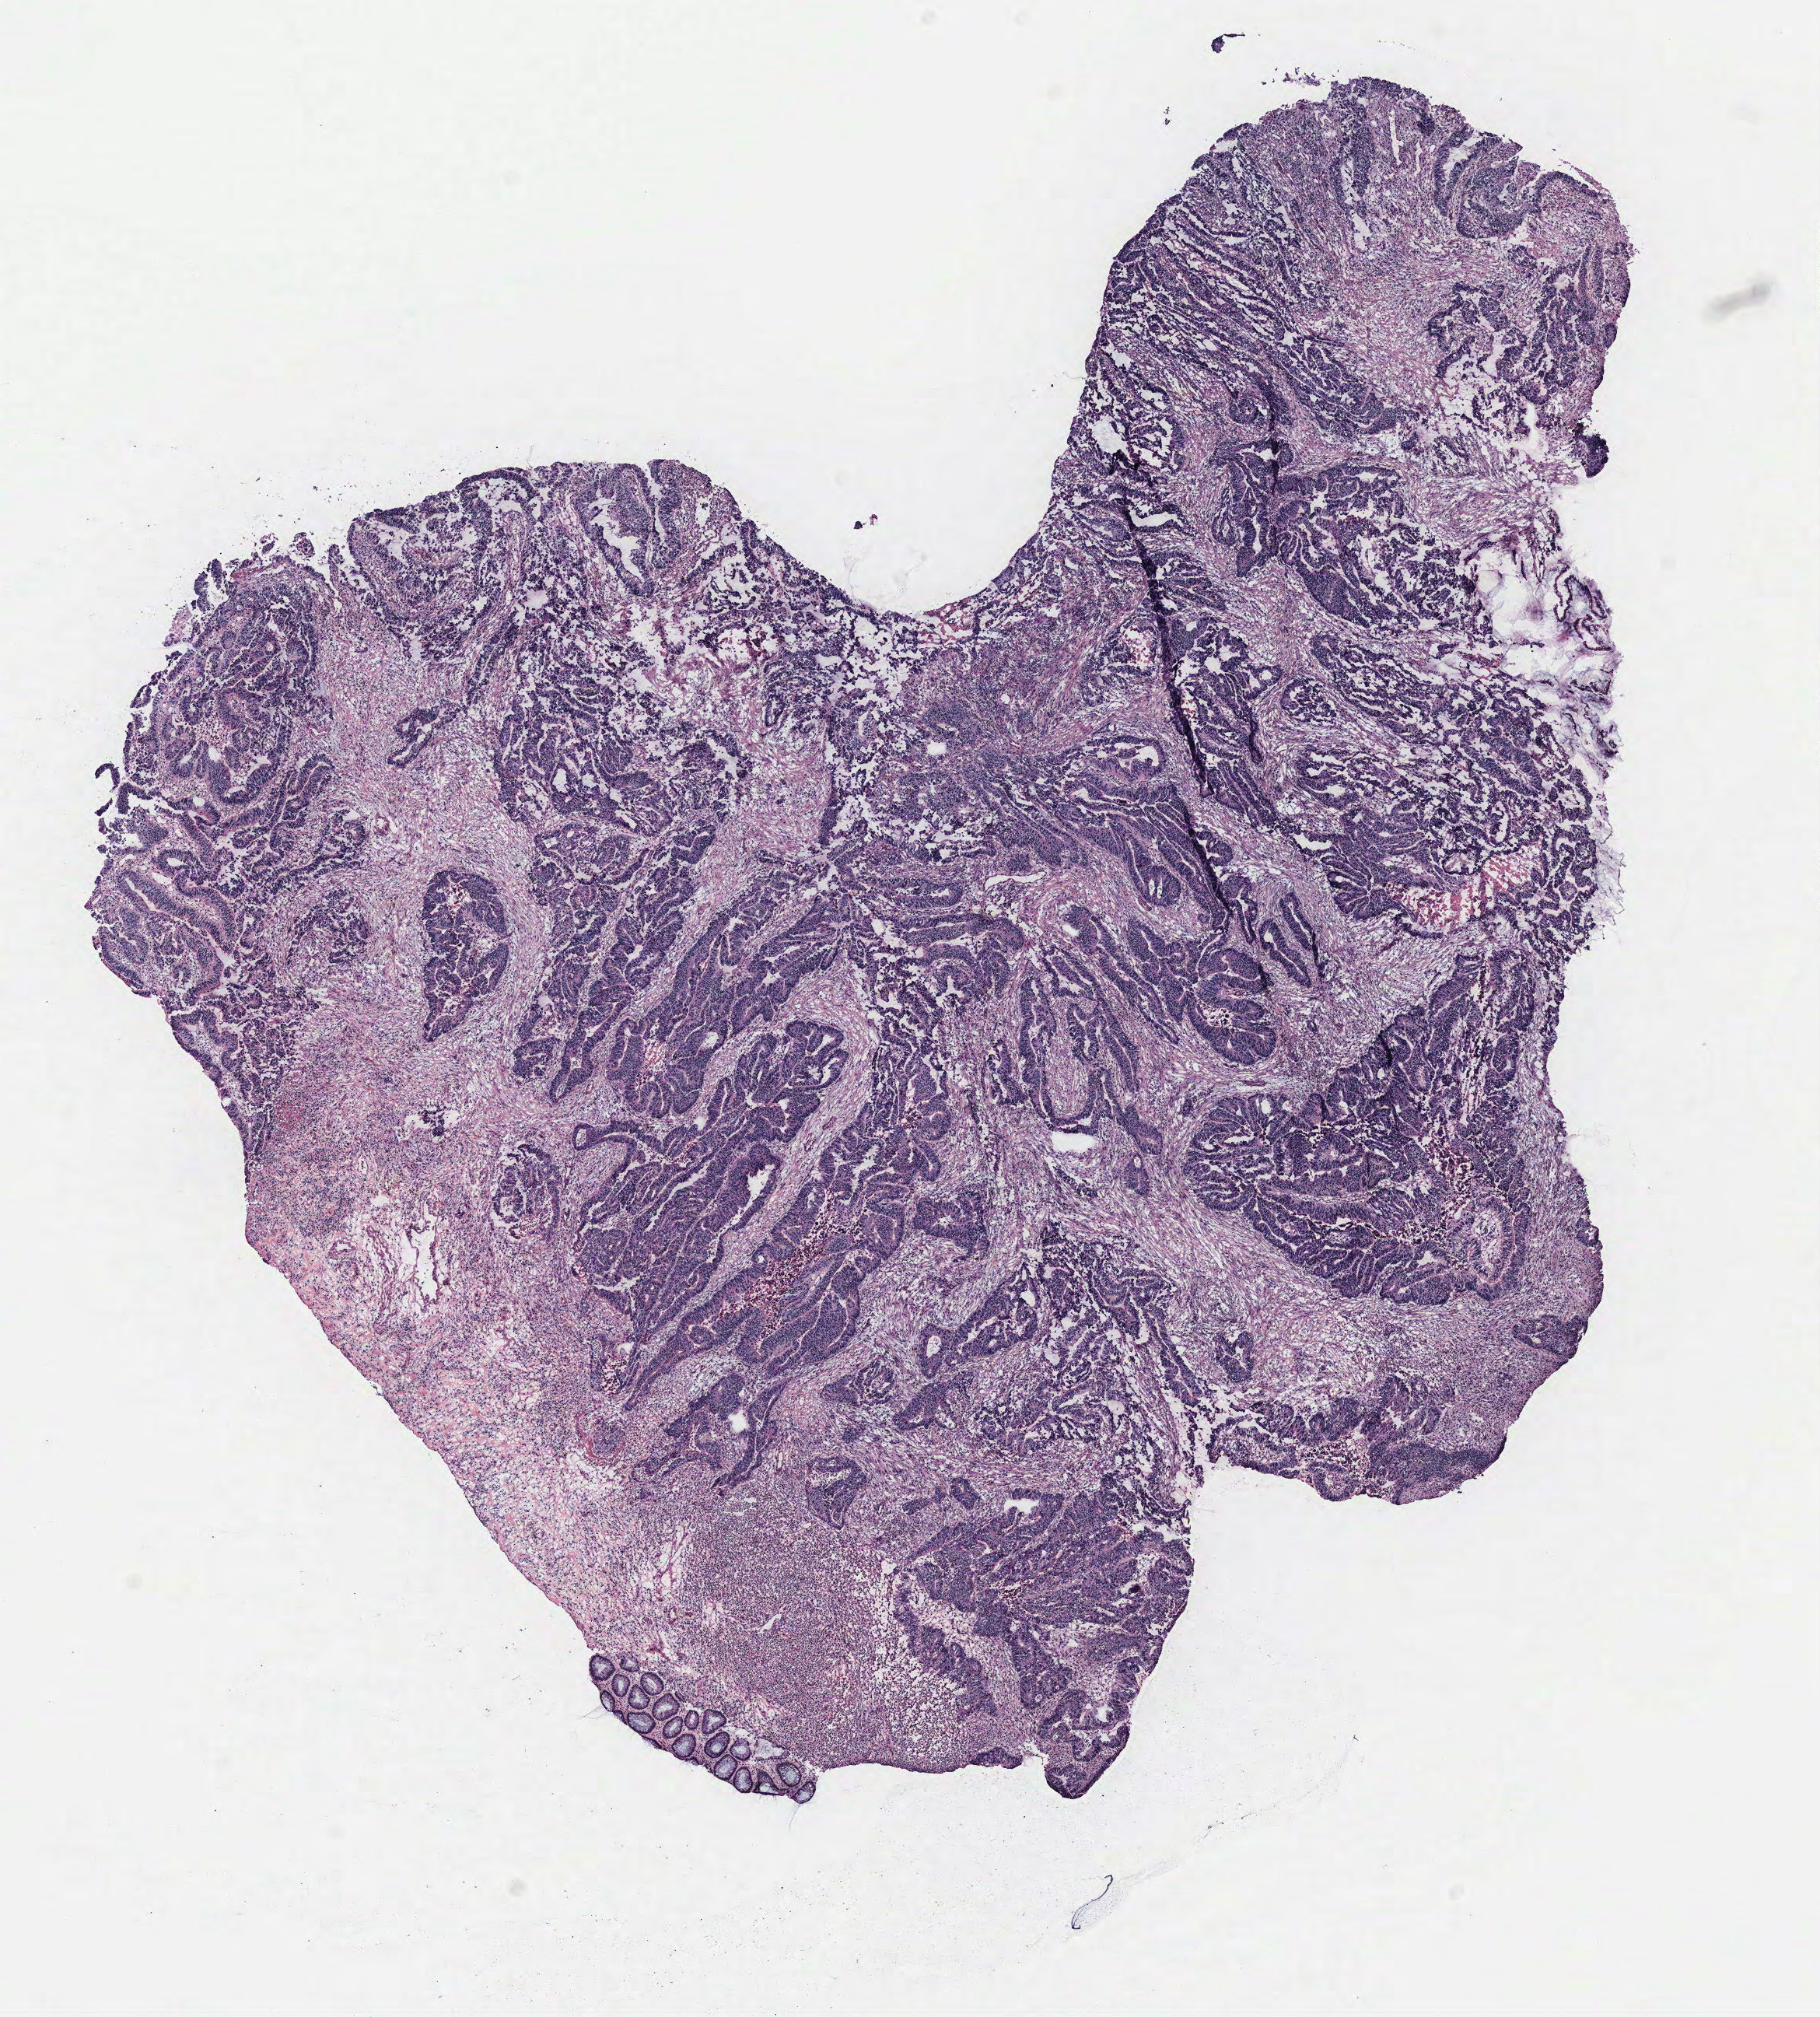
Digitized H&E tissue section (whole slide) — whole scanned area (about 9.4 x 10.4 mm, slide scanned at 40x) shown as a low-resolution overview, colon, tissue type not recorded. Male patient.
- patient diagnosis: Adenocarcinoma, NOS